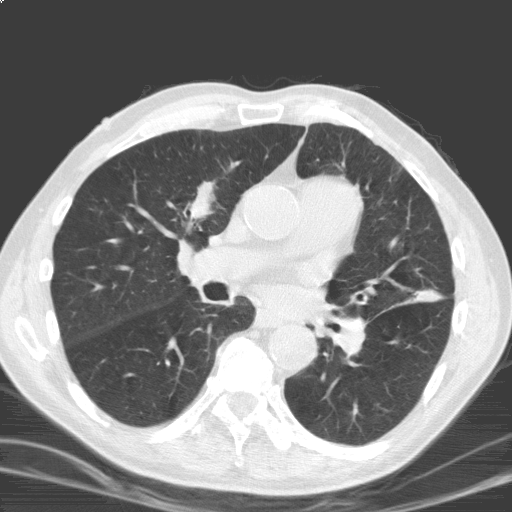
Low-dose screening chest CT, axial slice, second screening round (one year after baseline), lung window (W 1500 / L -600 HU), 3.2 mm slice thickness, standard (soft-tissue) reconstruction kernel (C), 120 kVp, slice 85 of 184 in the series, 512 × 512 image matrix. Male, age 69 years at enrolment. Current smoker at enrolment.
• Expert reader's lesion annotation, bounding box (x1, y1, x2, y2) in pixels: (174, 176, 231, 231).
• The screening reader recorded 2 non-calcified nodules or masses ≥4 mm on this exam (right upper lobe, left lower lobe); which of them this box marks is not recorded.
• Official screen result: positive, other.